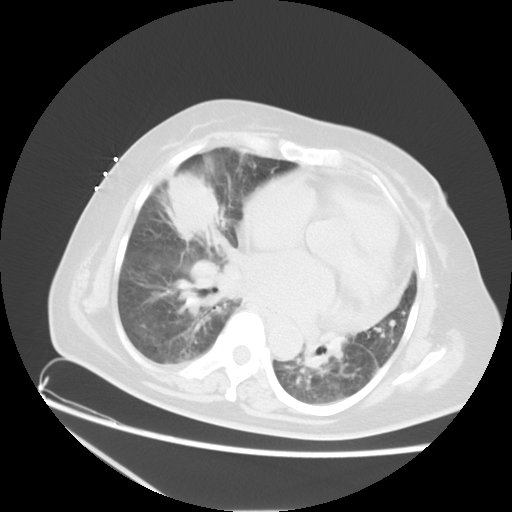
Chest CT, one axial slice; position 9 of 22 along the scan axis; lung window (W 1500 / L -600 HU); 5 mm slice thickness; 512 × 512 image matrix. Patient: female, 67 years. From the clinical record (not read from this slice): clinical TNM (as recorded): T2a N3 M1a.
Structures marked on this image (rectangle marked by the reading radiologist):
- lung tumour (recorded histology: adenocarcinoma): bounding box [x1, y1, x2, y2] px = [167, 168, 222, 241]